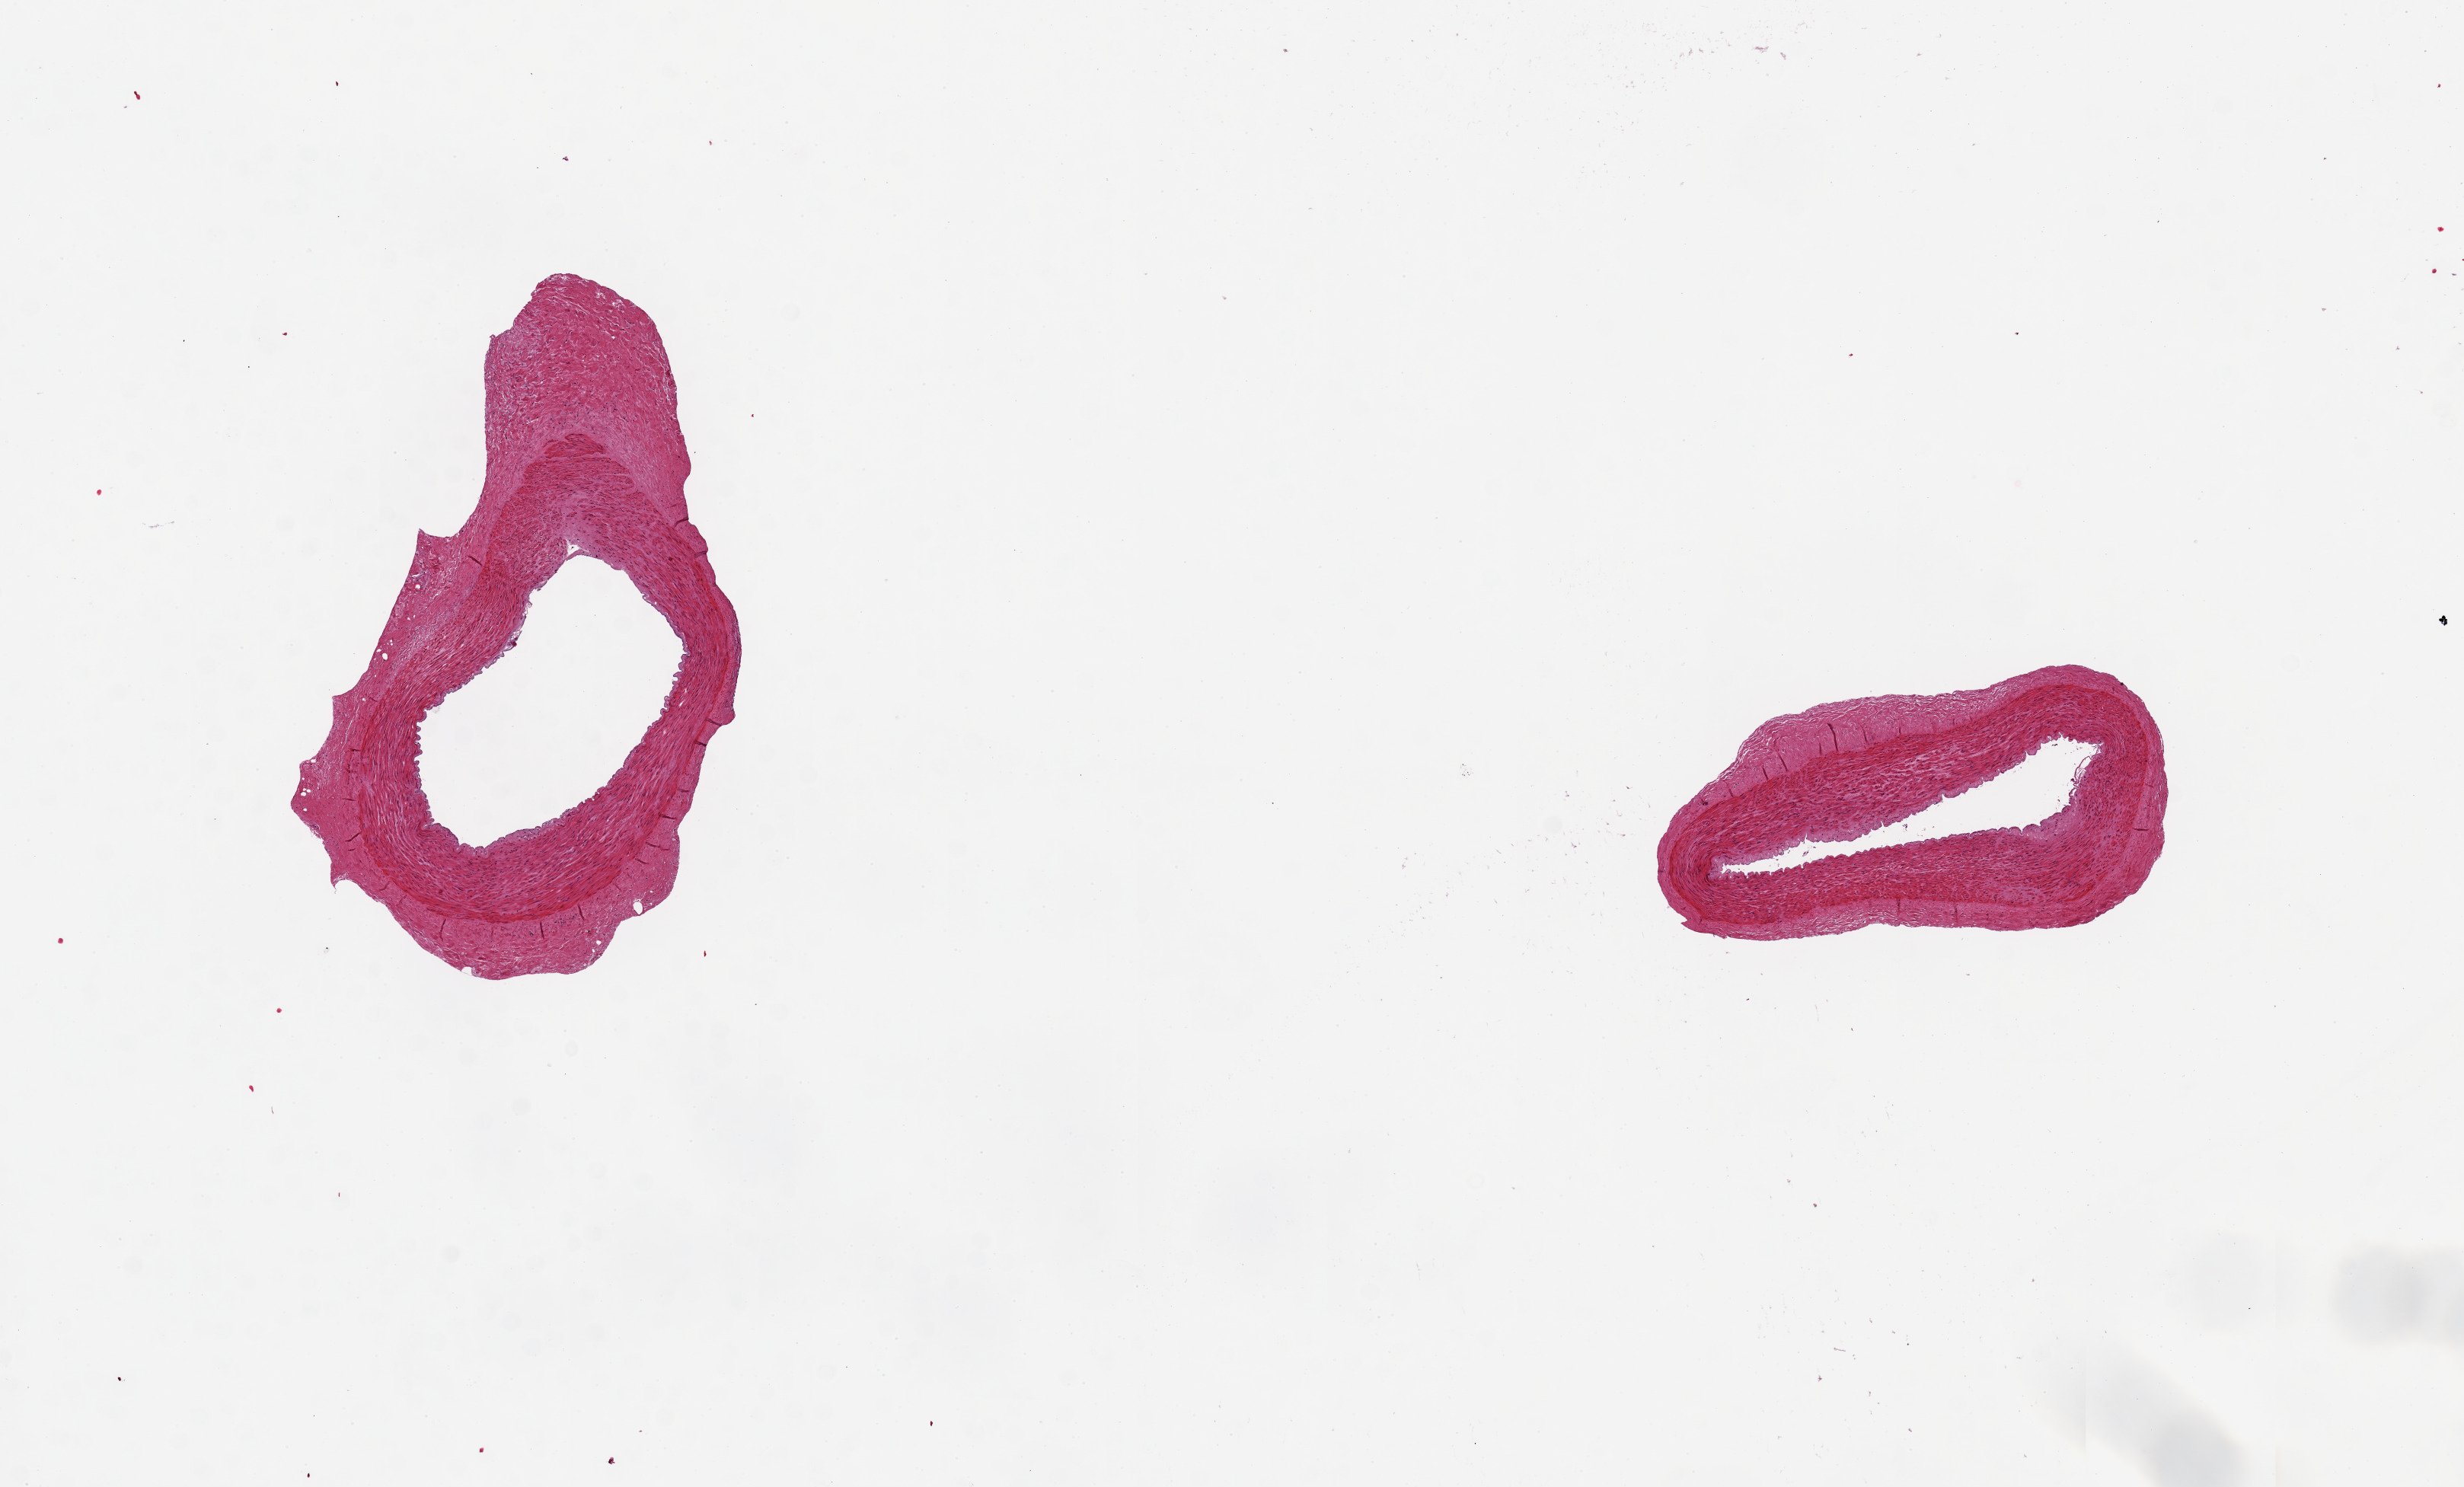
Whole-slide image, hematoxylin and eosin (H&E) stain, brightfield, whole scanned area (about 12.8 x 7.7 mm, from a 20x scan) shown as a low-resolution overview. PAXgene-fixed, paraffin-embedded tissue. Section of tibial artery (target tissue). Tissue donor sample. Donor: male.
Pathologist's review note for this sample: 2 pieces, ~ 2 mm diameter; artery no extraneous adipose.